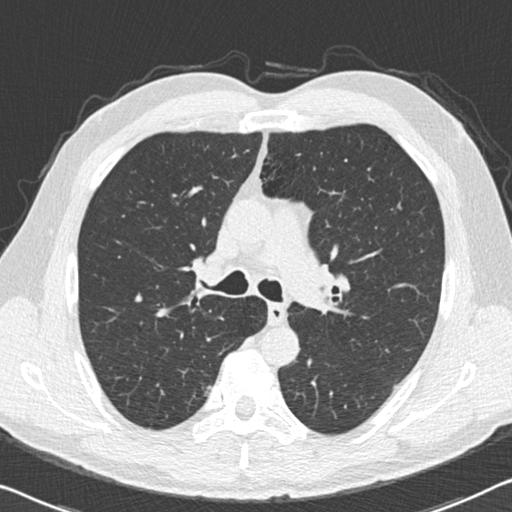
Chest CT (low-dose screening protocol), one axial image; second annual screen; lung window (W 1500 / L -600 HU); 2 mm slice thickness; standard (soft-tissue) reconstruction kernel (B30f); 120 kVp; slice 63 of 179 in the series; 512 × 512 image matrix. Male, age 55 years at enrolment. Current smoker at enrolment.
- Expert reader's lesion annotation, bounding box <191,373,224,407> (left, top, right, bottom; pixels).
- Screening reader's record for this exam: no non-calcified nodule ≥4 mm recorded.
- Official screen result: negative screen, minor abnormalities not suspicious for lung cancer.
- Later outcome: lung cancer diagnosed 641 days after this screen — adenocarcinoma, NOS, right upper lobe, poorly differentiated (G3), stage IA (AJCC 6th edition), 15 mm at pathology.